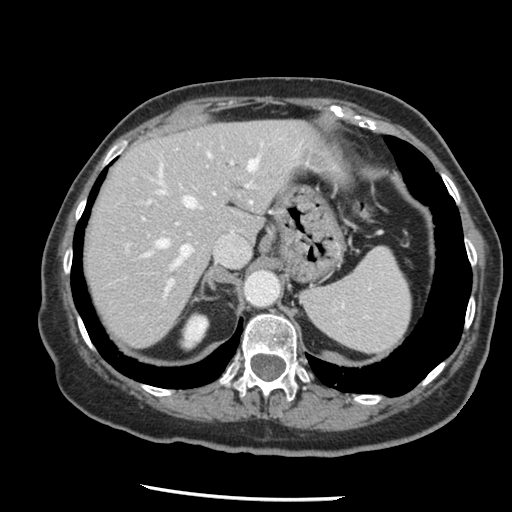
Contrast-enhanced abdominal CT, one axial slice; reconstruction kernel STANDARD; 120 kVp; intravenous contrast given; soft-tissue window (W 400 / L 40 HU); 2.5 mm slice thickness; 512 × 512 image matrix, field of view 330 × 330 mm. Female patient, age 85 years. Case-level facts recorded for this patient, not image findings: diagnosis: colorectal cancer liver metastases, imaged before liver resection; multiple liver metastases: no; largest metastasis: 0.9 cm; disease in both lobes: no.
Structures marked on this image (manually delineated by an expert):
- hepatic veins: bounding box [x1, y1, x2, y2] px = [145, 140, 265, 267]
- liver: [84, 121, 316, 347]
- planned liver remnant (the part of the liver to remain after resection): [84, 121, 316, 347]
- portal vein (with intrahepatic branches): [128, 165, 251, 298]